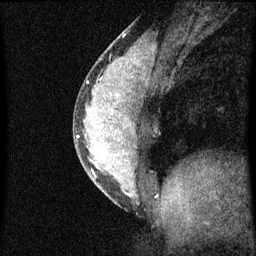
Breast MRI (dynamic contrast-enhanced), one sagittal slice. Slice 25 of 60 in the series (ordered by position). Dynamic contrast-enhanced series, image 2 of 3 at this slice position (ordered by acquisition). 1.5 T. TE 4.2 ms, TR 8 ms. 256 × 256 image matrix. Female patient, age 33 years.
Outlined on this slice (semi-automatic segmentation, software-assisted and operator-edited):
- analysis volume of interest (the breast-tissue region the enhancement analysis was run in; not a lesion): bounding box (x1, y1, x2, y2) in pixels: (74, 56, 155, 207)
- tumour enhancement mask (voxels above the 70 % enhancement threshold inside the analysis volume of interest): (77, 60, 135, 197)